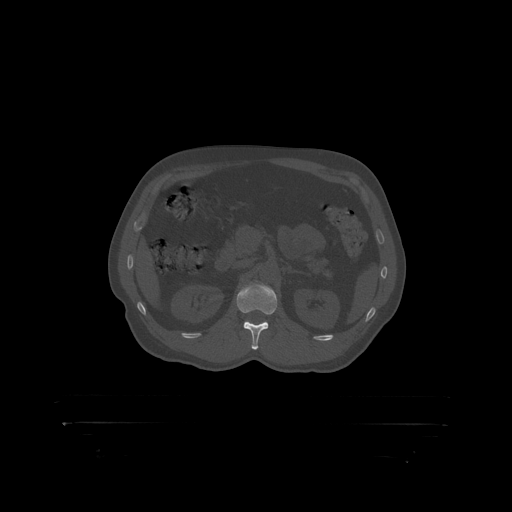
CT including the spine, one axial slice. Position 319 of 399 along the scan axis. Reconstruction kernel STANDARD. Bone window (W 1800 / L 400 HU). 1.25 mm slice thickness. 512 × 512 image matrix, field of view 650 × 650 mm. Male patient, age 46 years. Case-level facts recorded for this patient, not image findings: primary cancer: skin.
Outlined on this slice (semi-automatically segmented with operator editing):
- L1 vertebra: box from (x=237, y=283) to (x=278, y=315) px